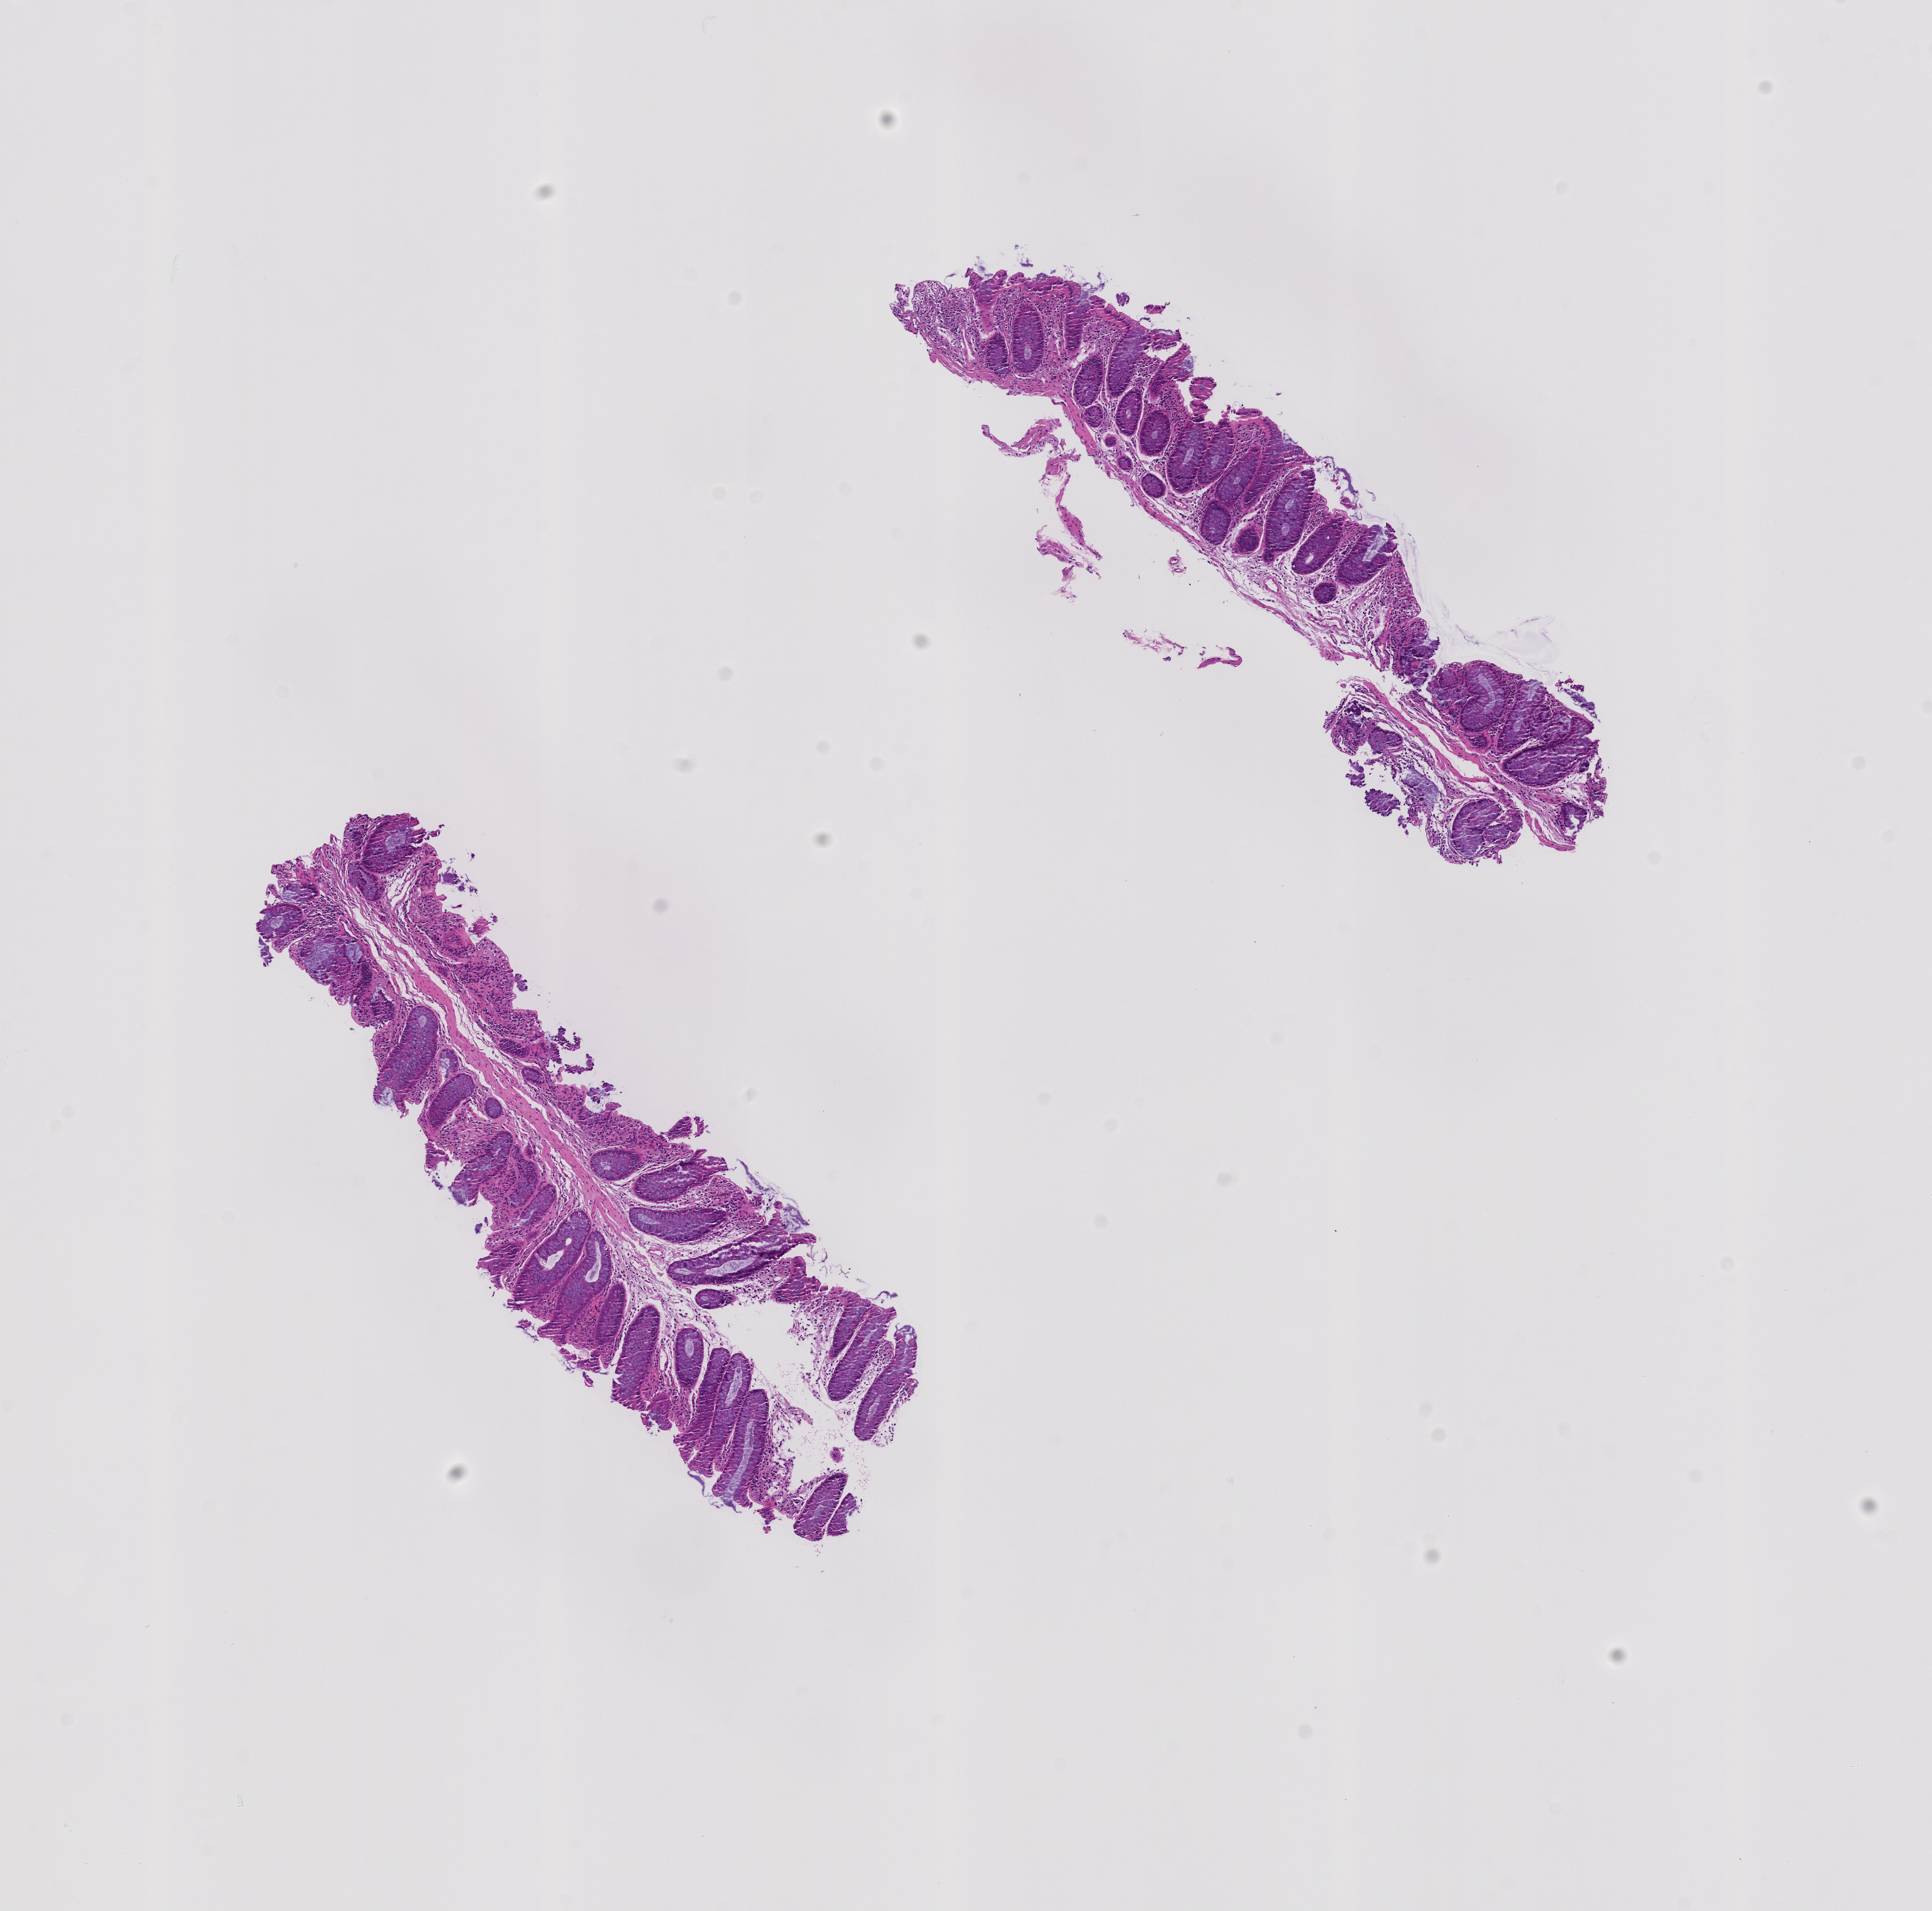
Whole-slide image, haematoxylin and eosin stain: colon biopsy, whole scanned area (about 6.2 x 6.1 mm) shown as a low-resolution overview; formalin-fixed paraffin-embedded section; site: sigmoid colon. Patient sex: female.
Lesion category (as recorded): hyperplasia.